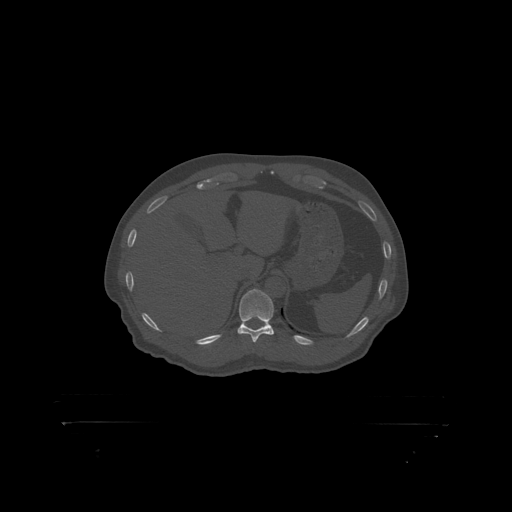
CT including the spine, one axial slice. Position 376 of 399 along the scan axis. Reconstruction kernel STANDARD. 120 kVp. Bone window (W 1800 / L 400 HU). 1.25 mm slice thickness. 512 × 512 image matrix, field of view 650 × 650 mm. Male patient, age 46 years. Case-level facts recorded for this patient, not image findings: primary cancer: skin.
Outlined on this slice (semi-automatically segmented with operator editing):
- T11 vertebra: box from (x=239, y=289) to (x=274, y=319) px